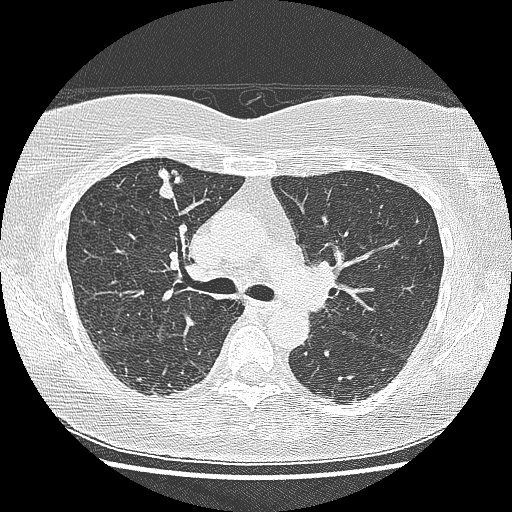
Low-dose screening chest CT, one axial slice. Slice 96 of 155 in the series (ordered by position). Lung window (W 1500 / L -600 HU). 2.5 mm slice thickness. 512 × 512 image matrix, field of view 330 × 330 mm.
Structures marked on this image (outlined manually by an expert reader):
- lesion 1 (tumor, upper lobe of right lung): box from (x=155, y=166) to (x=183, y=199) px